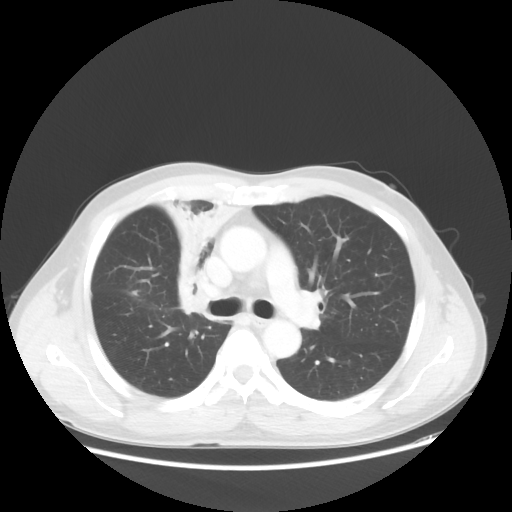
Chest CT, one axial slice. Slice 34 of 56 in the series (ordered by position). 100 kVp. Lung window (W 1500 / L -600 HU). 512 × 512 image matrix, field of view 398 × 398 mm. Male patient, age 60 years. Case-level facts recorded for this patient, not image findings: clinical TNM (as recorded): T2a N1 M0.
Annotated regions visible in this slice (bounding box drawn by a radiologist):
- lung tumour (recorded histology: squamous cell carcinoma): bounding box (x1, y1, x2, y2) in pixels: (139, 180, 240, 316)